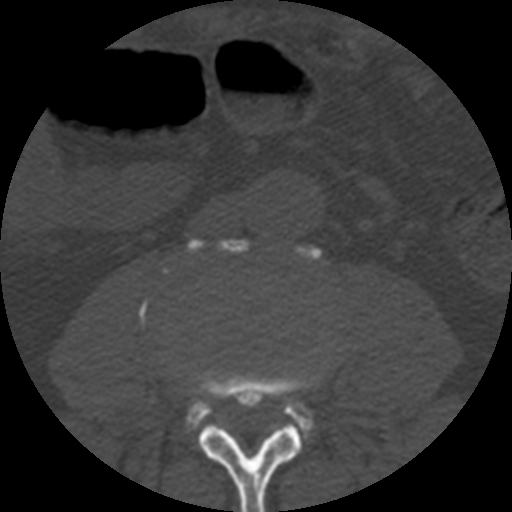
CT including the spine, one axial slice; slice 109 of 508 in the series (ordered by position); reconstruction kernel STANDARD; 120 kVp; bone window (W 1800 / L 400 HU); 1.25 mm slice thickness; 512 × 512 image matrix. Patient age 57 years. From the clinical record (not read from this slice): primary cancer: prostate.
Annotated regions visible in this slice (semi-automatically segmented with operator editing):
- L3 vertebra: bounding box [x1, y1, x2, y2] px = [177, 362, 325, 512]
- L4 vertebra: [140, 239, 321, 442]